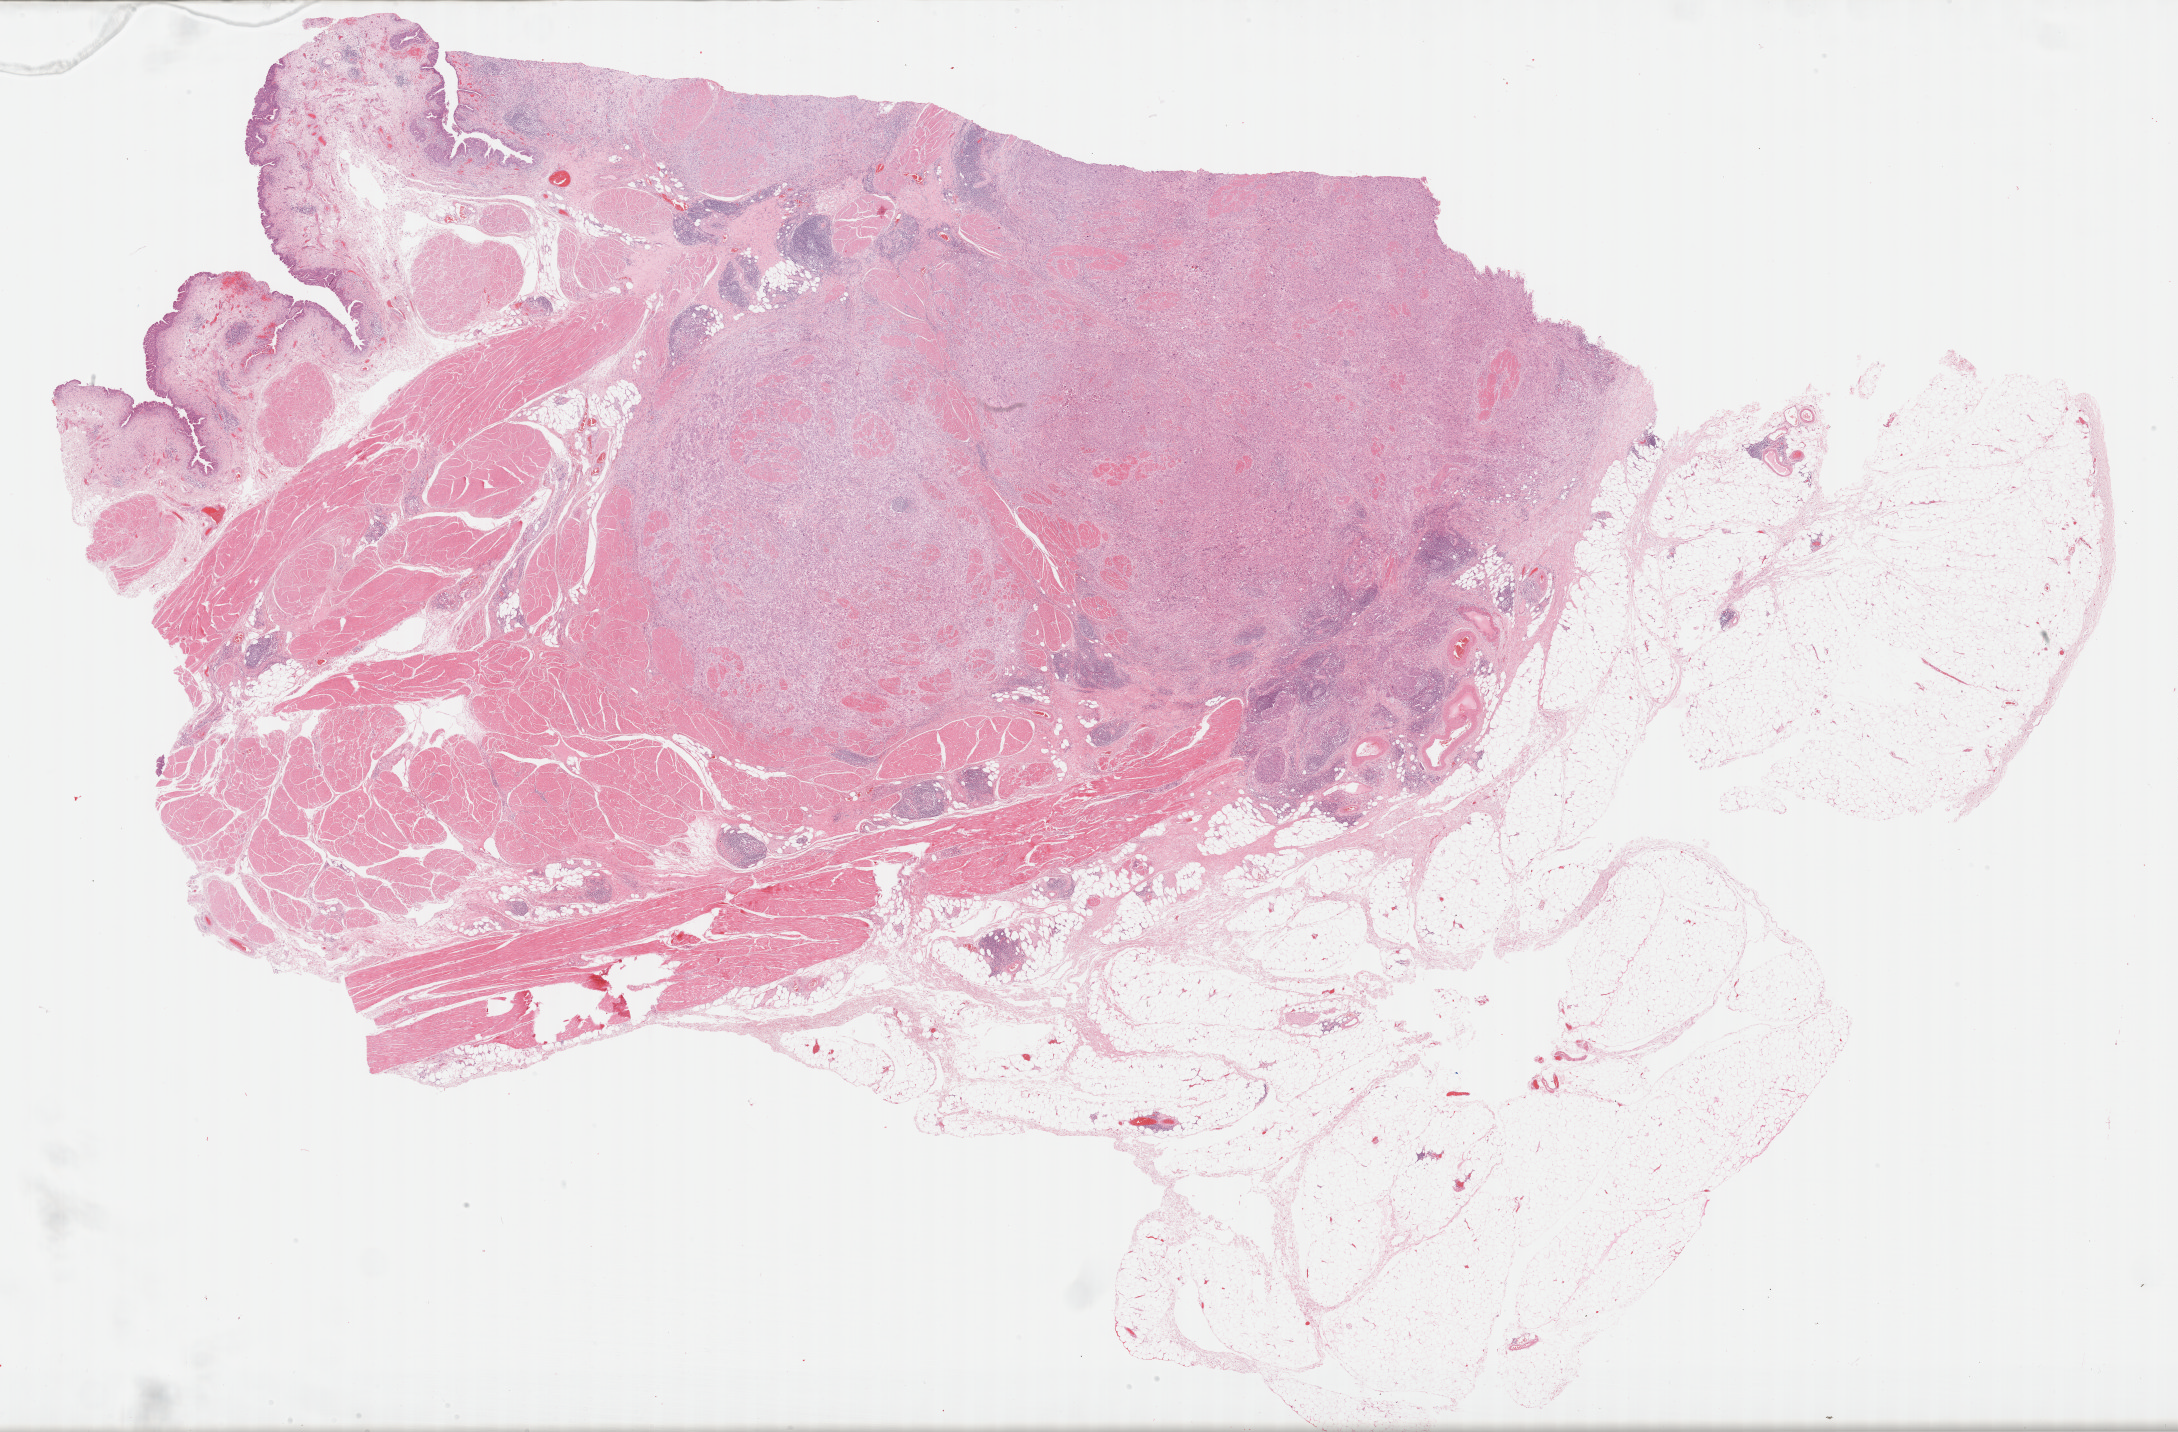
Digitized H&E tissue section (whole slide) — a low-resolution overview of the entire scanned area, about 35.2 x 23.2 mm; formalin-fixed paraffin-embedded (FFPE) diagnostic section; sample: primary tumour, bladder. Patient: female, age at initial diagnosis 60 years.
Pathologic diagnosis: Transitional cell carcinoma.